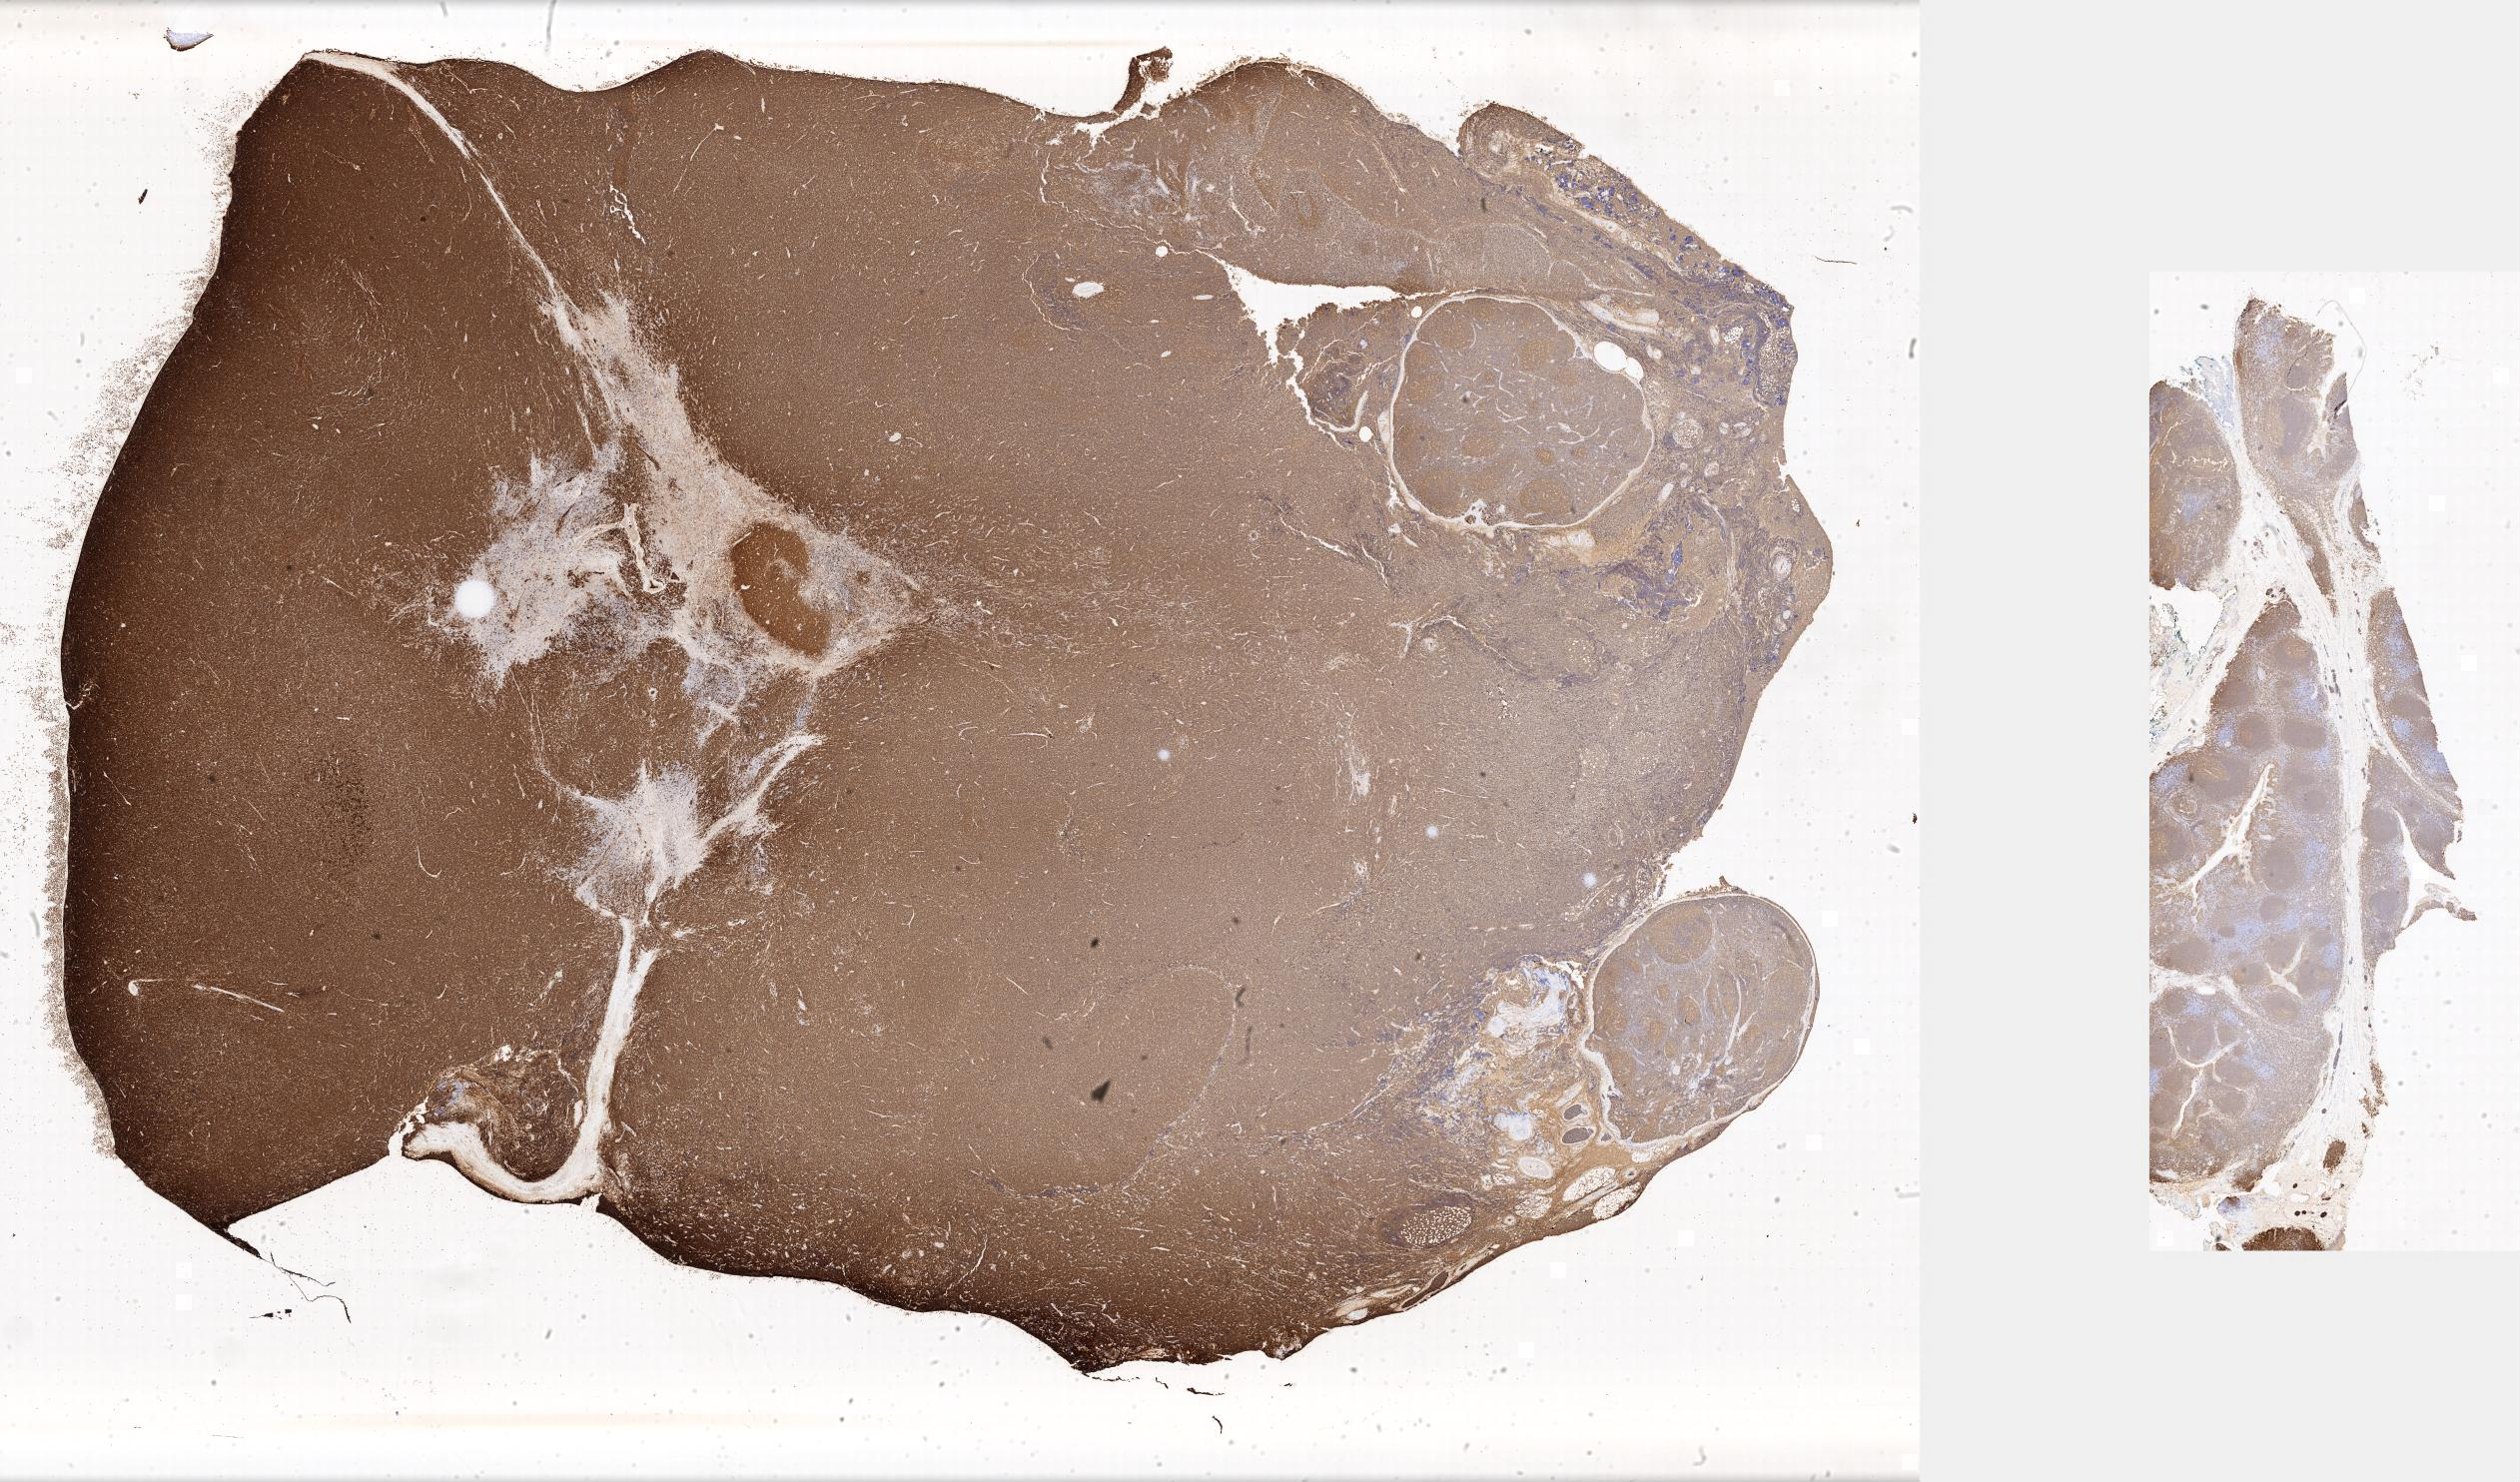
Immunohistochemistry (IHC) whole-slide image stained for CD20 — a low-resolution overview of the entire scanned area; tumor tissue; site: lymph node of head and neck. Male, age 3 years at initial diagnosis.
Histologic diagnosis: Burkitt lymphoma, NOS.